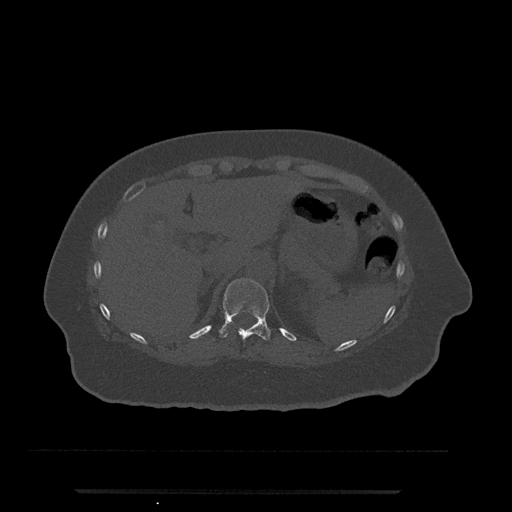
CT including the spine, one axial slice. Slice 229 of 797 in the series (ordered by position). Reconstruction kernel Br40s/3. 120 kVp. Bone window (W 1800 / L 400 HU). 512 × 512 image matrix, field of view 440 × 440 mm. Female patient, age 51 years. From the clinical record (not read from this slice): primary cancer: neuro.
Structures marked on this image (semi-automatically segmented with operator editing):
- T11 vertebra: bounding box (x1, y1, x2, y2) in pixels: (219, 278, 271, 341)